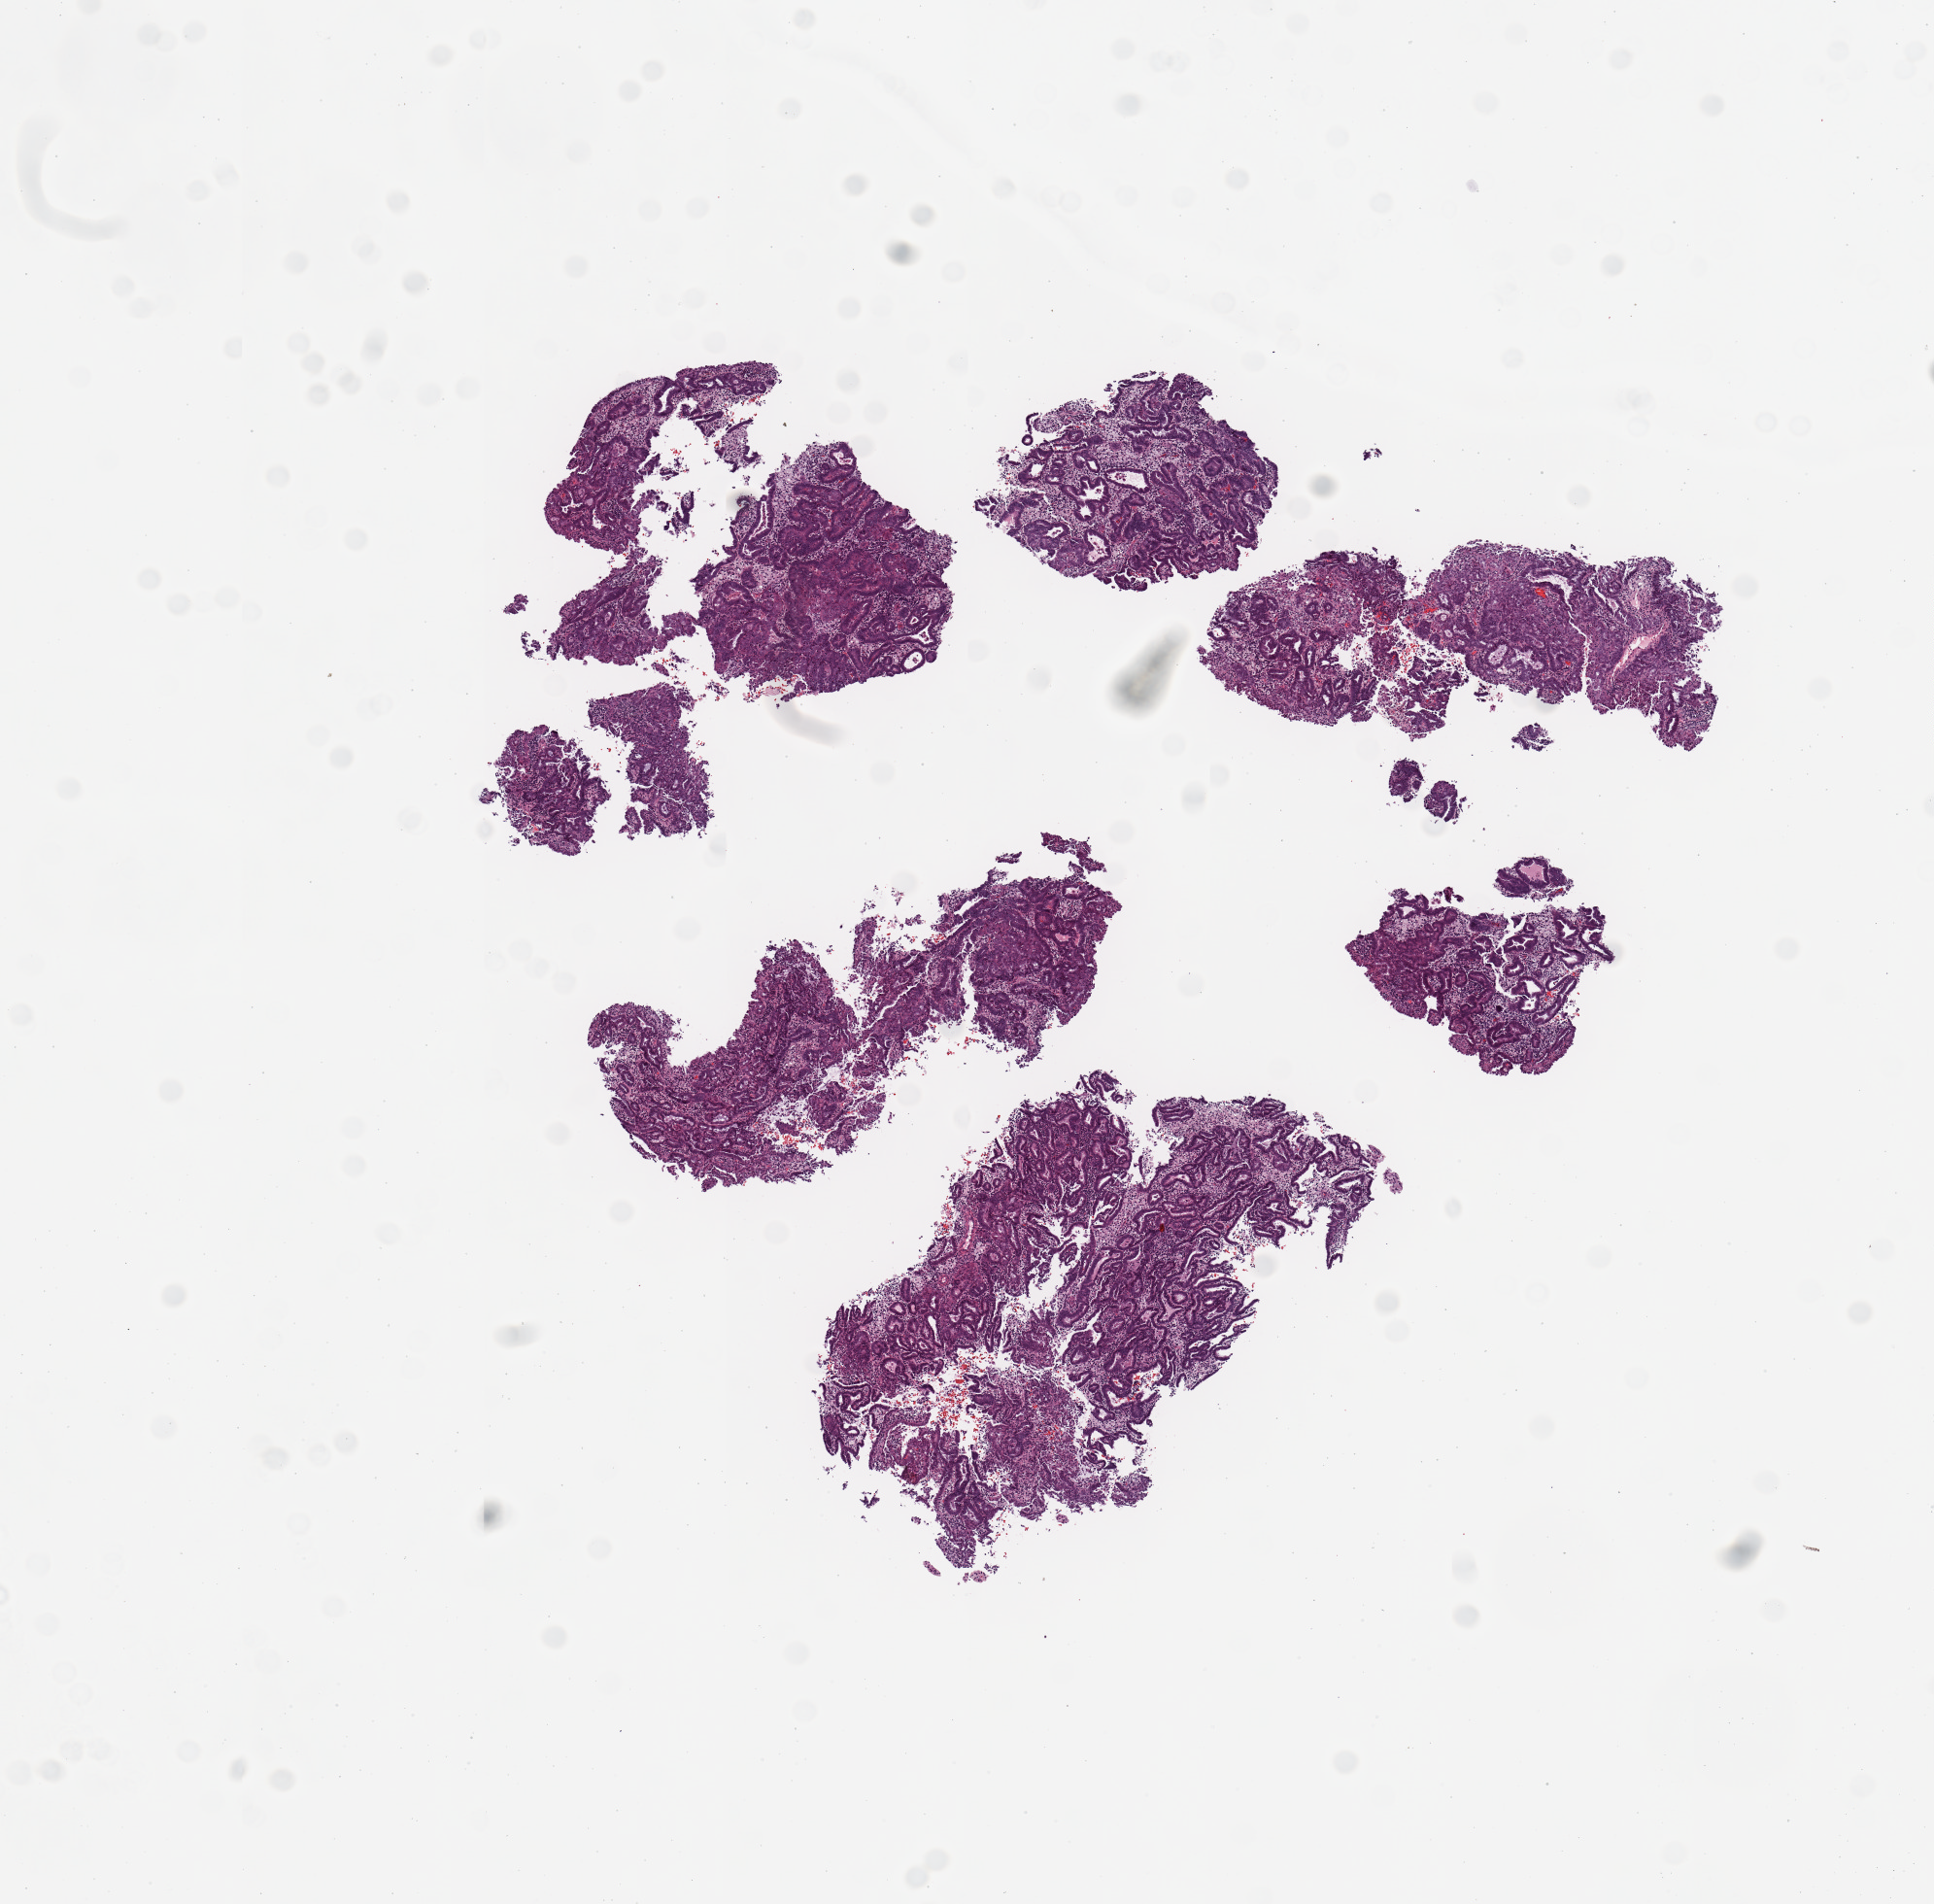
Whole-slide histology image, H&E-stained, whole scanned area (about 7.9 x 7.8 mm, slide scanned at 20x) shown as a low-resolution overview. Tumour tissue sample, sampled site: uterus. 69-year-old female patient. Histologic grade: G1 (well differentiated). Slide review estimates, as recorded: tumour nuclei 85%, necrosis 2%.
Diagnosis: Endometrioid adenocarcinoma, NOS. AJCC pathologic stage: I.